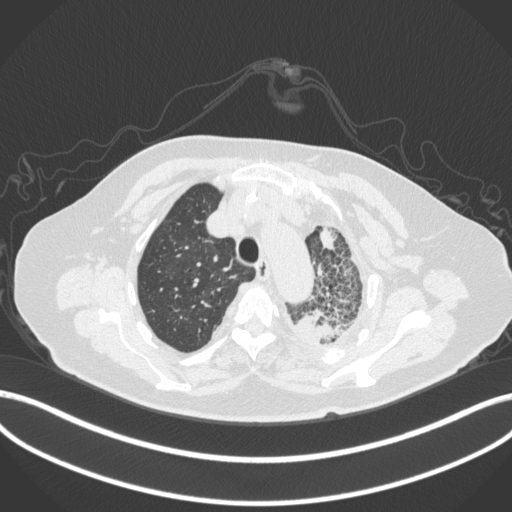
Chest CT, one axial slice. Position 314 of 399 along the scan axis. Reconstruction kernel B31f. 120 kVp. Lung window (W 1500 / L -600 HU). 1 mm slice thickness. 512 × 512 image matrix, field of view 400 × 400 mm. Patient: female, 75 years. Case-level facts recorded for this patient, not image findings: clinical TNM (as recorded): T3 N3 M1.
Annotated regions visible in this slice (bounding box drawn by a radiologist):
- lung tumour (recorded histology: adenocarcinoma): bounding box (x1, y1, x2, y2) in pixels: (296, 307, 343, 346)